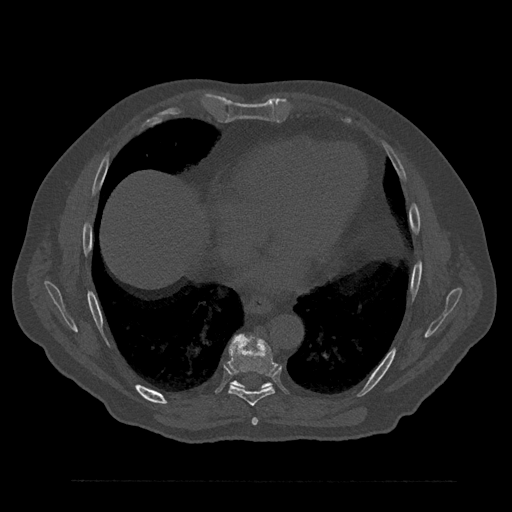
CT including the spine, one axial slice; position 444 of 797 along the scan axis; 120 kVp; bone window (W 1800 / L 400 HU); 0.5 mm slice thickness; 512 × 512 image matrix, field of view 430 × 430 mm. Patient: male, 61 years. From the clinical record (not read from this slice): primary cancer: prostate.
Annotated regions visible in this slice (semi-automatic segmentation, software-assisted and operator-edited):
- T7 vertebra: bounding box <252,418,258,425> (left, top, right, bottom; pixels)
- T8 vertebra: <227,335,278,406>
- T9 vertebra: <231,381,271,389>